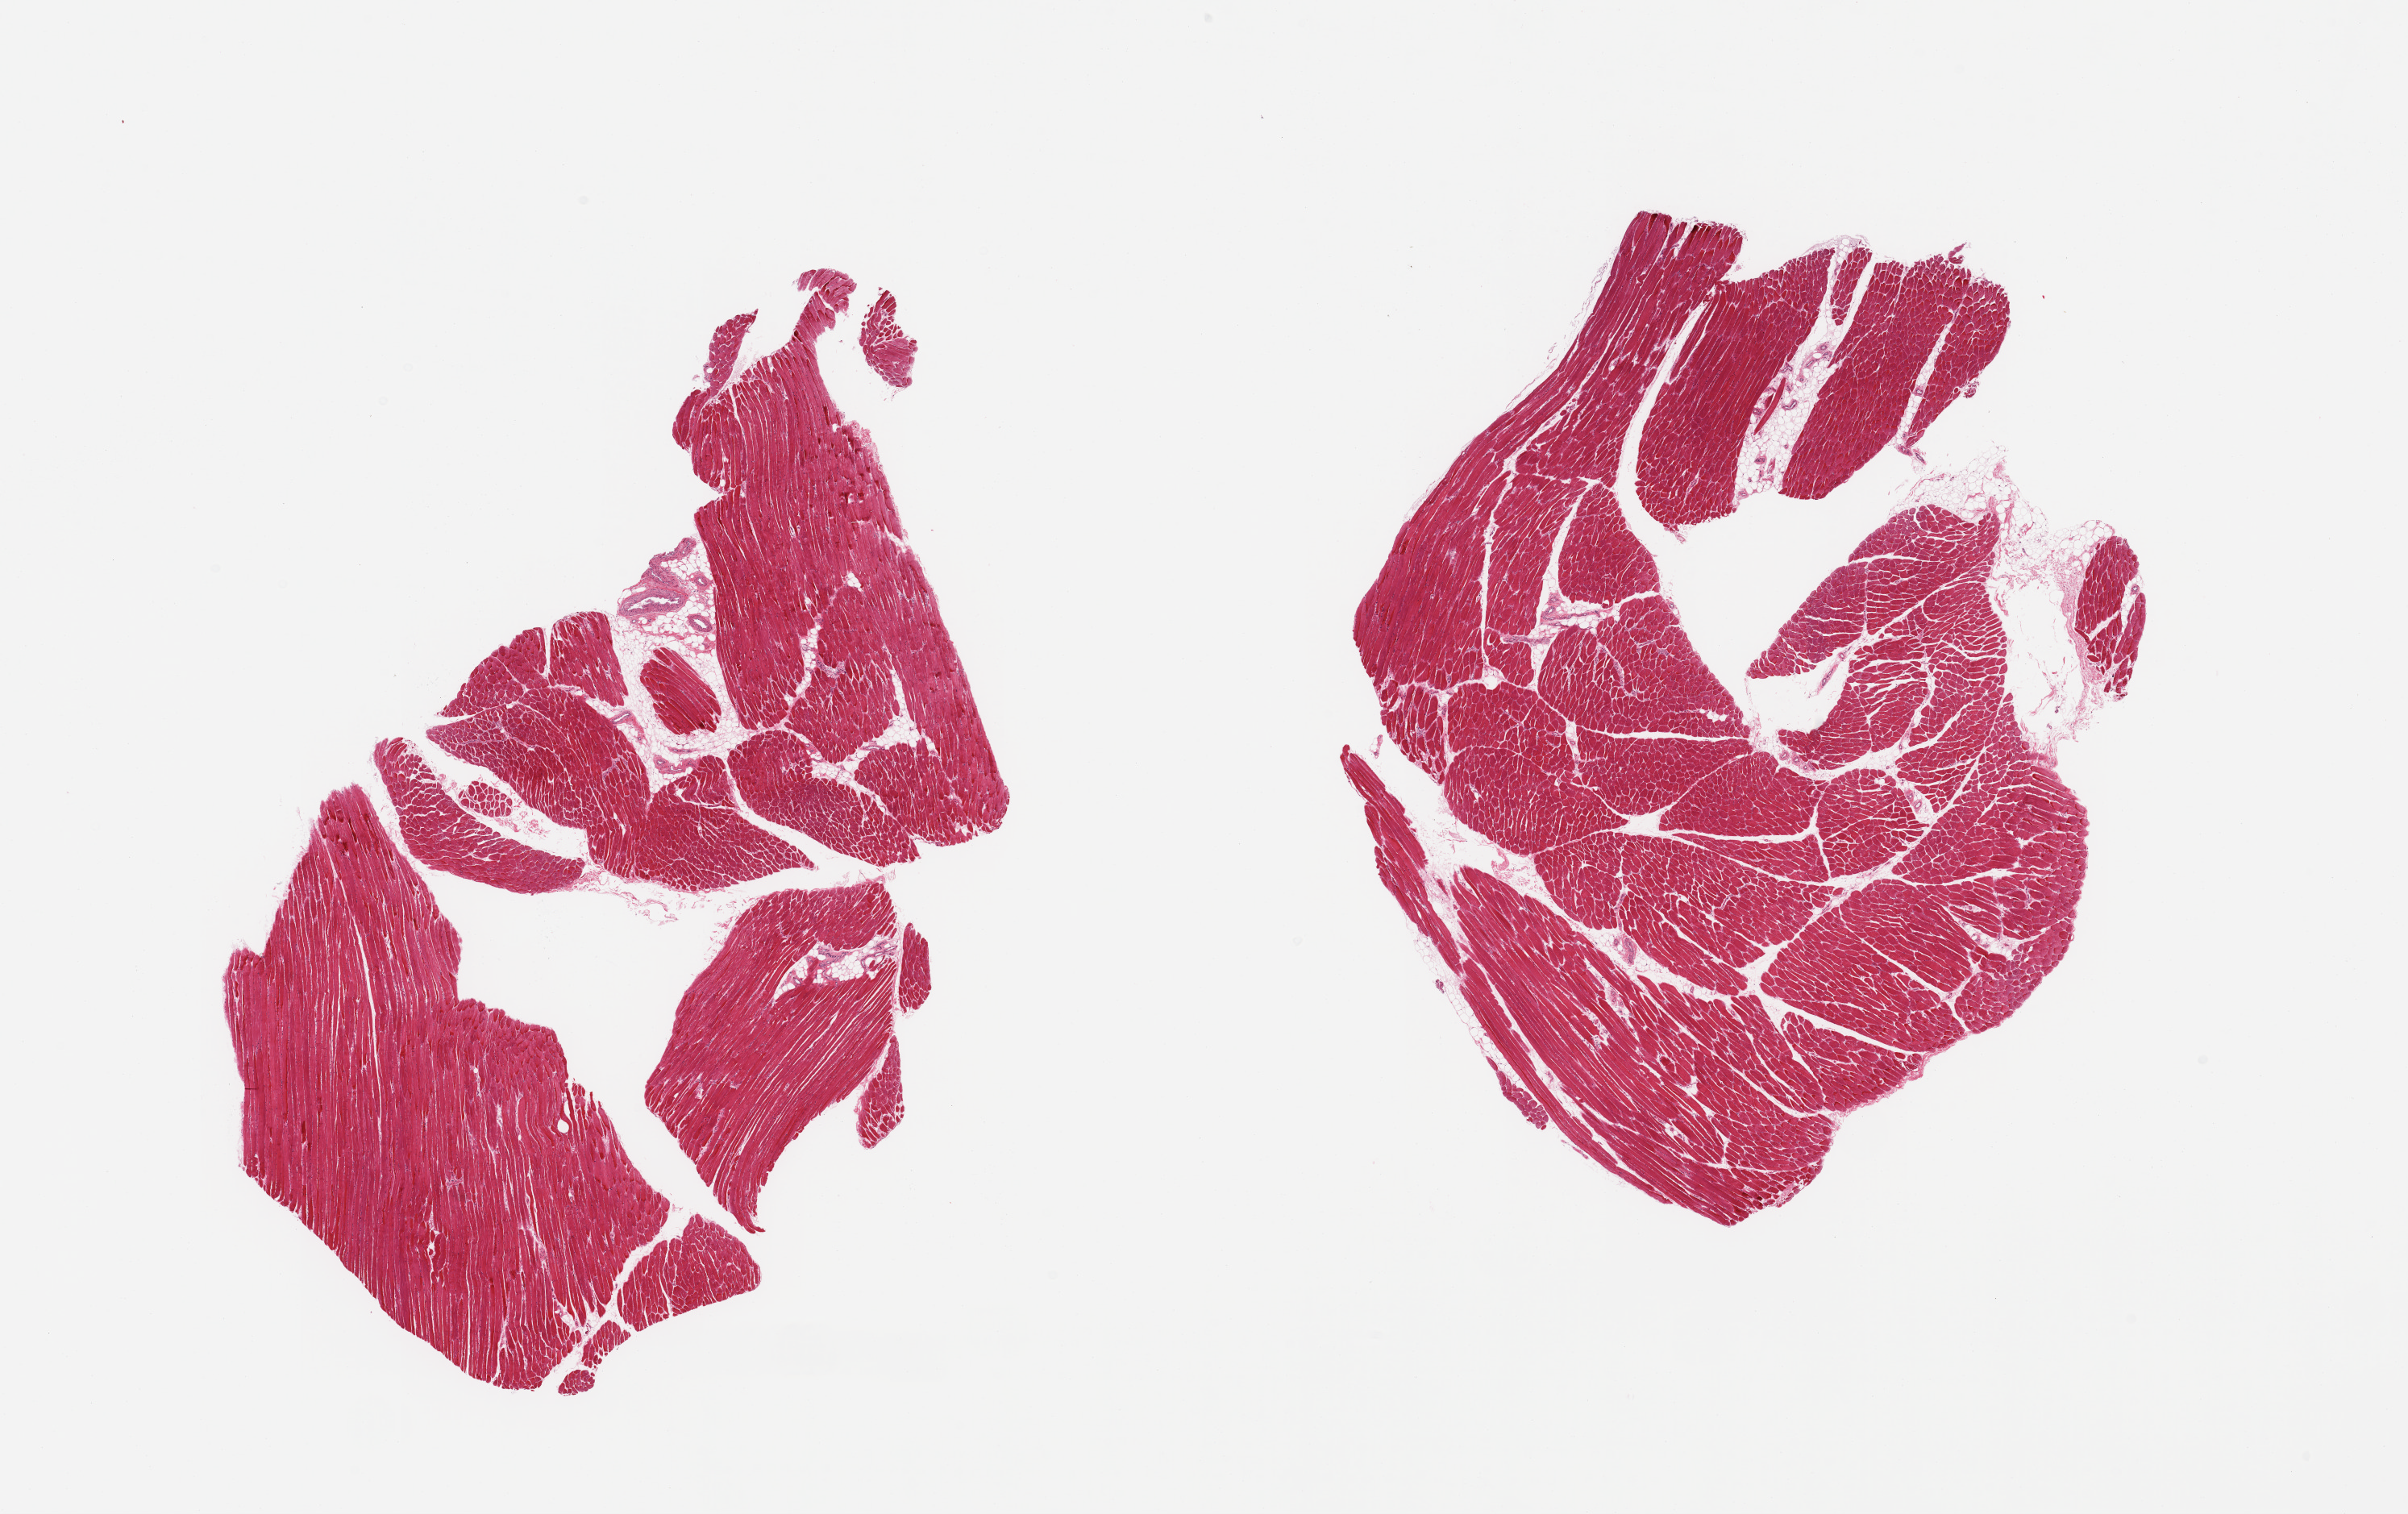
Whole-slide image, haematoxylin and eosin stain — shown as a low-resolution overview of the whole scanned area (about 23.6 x 14.9 mm, from a 20x scan); PAXgene-fixed, paraffin-embedded tissue; section of skeletal muscle (target tissue); donor tissue sample. Donor sex: male.
Pathologist's review note for this sample: 2 pieces; <5% internal fat.